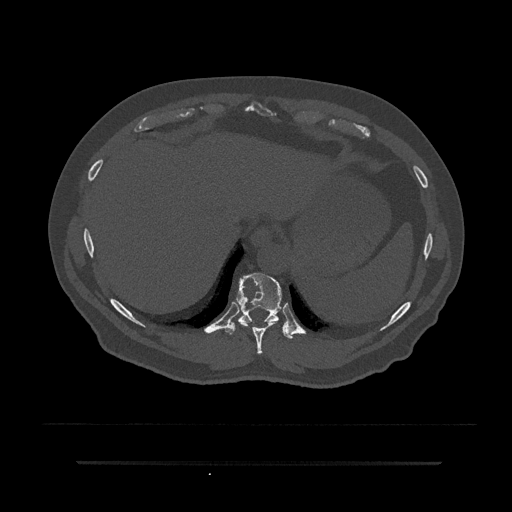
CT including the spine, one axial slice; position 350 of 797 along the scan axis; 120 kVp; bone window (W 1800 / L 400 HU); 0.5 mm slice thickness; 512 × 512 image matrix, field of view 464 × 464 mm. Patient: male, 59 years. Case-level facts recorded for this patient, not image findings: primary cancer: bile ducts; vertebrae with lytic lesions (as recorded): T10.
Annotated regions visible in this slice (semi-automatically segmented with operator editing):
- T10 vertebra: bounding box [x1, y1, x2, y2] px = [227, 273, 293, 339]
- T9 vertebra: [242, 323, 273, 354]